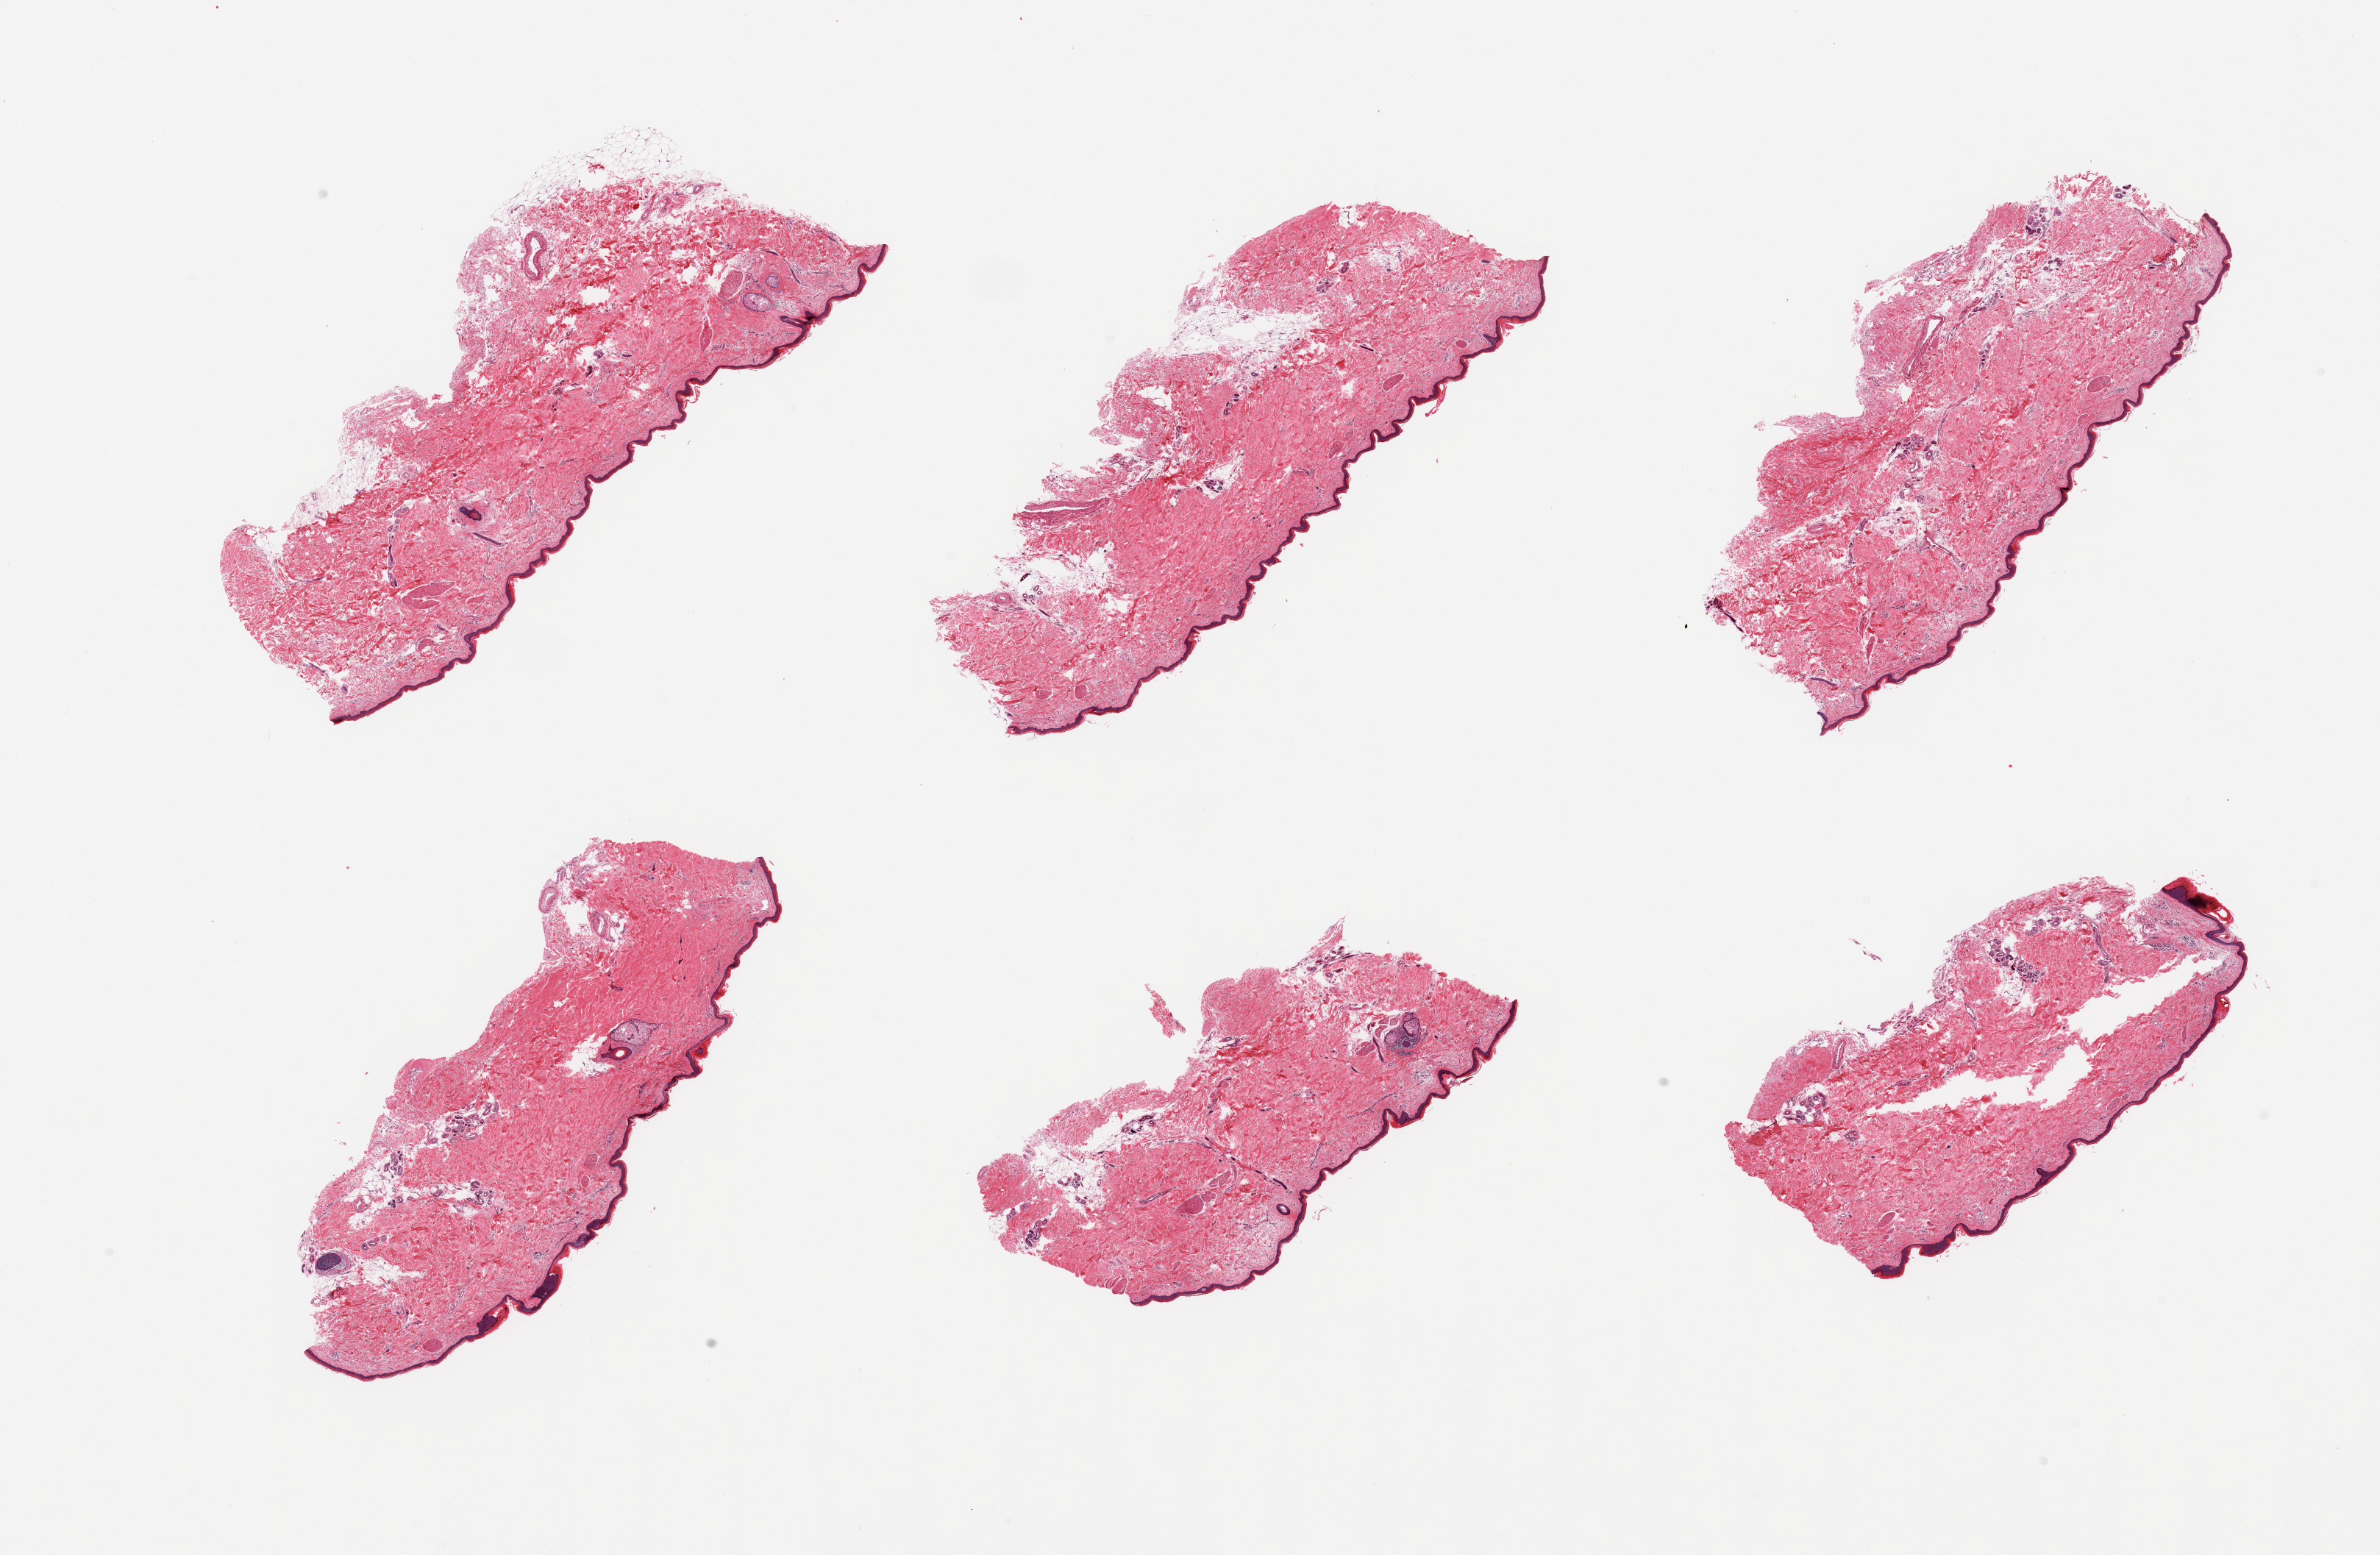
Digitized haematoxylin and eosin-stained section, a low-resolution overview of the entire scanned area, about 25.6 x 16.7 mm (from a 20x scan), PAXgene-fixed, paraffin-embedded tissue, section of skin of lower leg (target tissue), tissue donor sample. Donor: male.
Pathologist's review note for this sample: 6 pieces; well trimmed; 10% dermal fat; foci of benign keratosis.